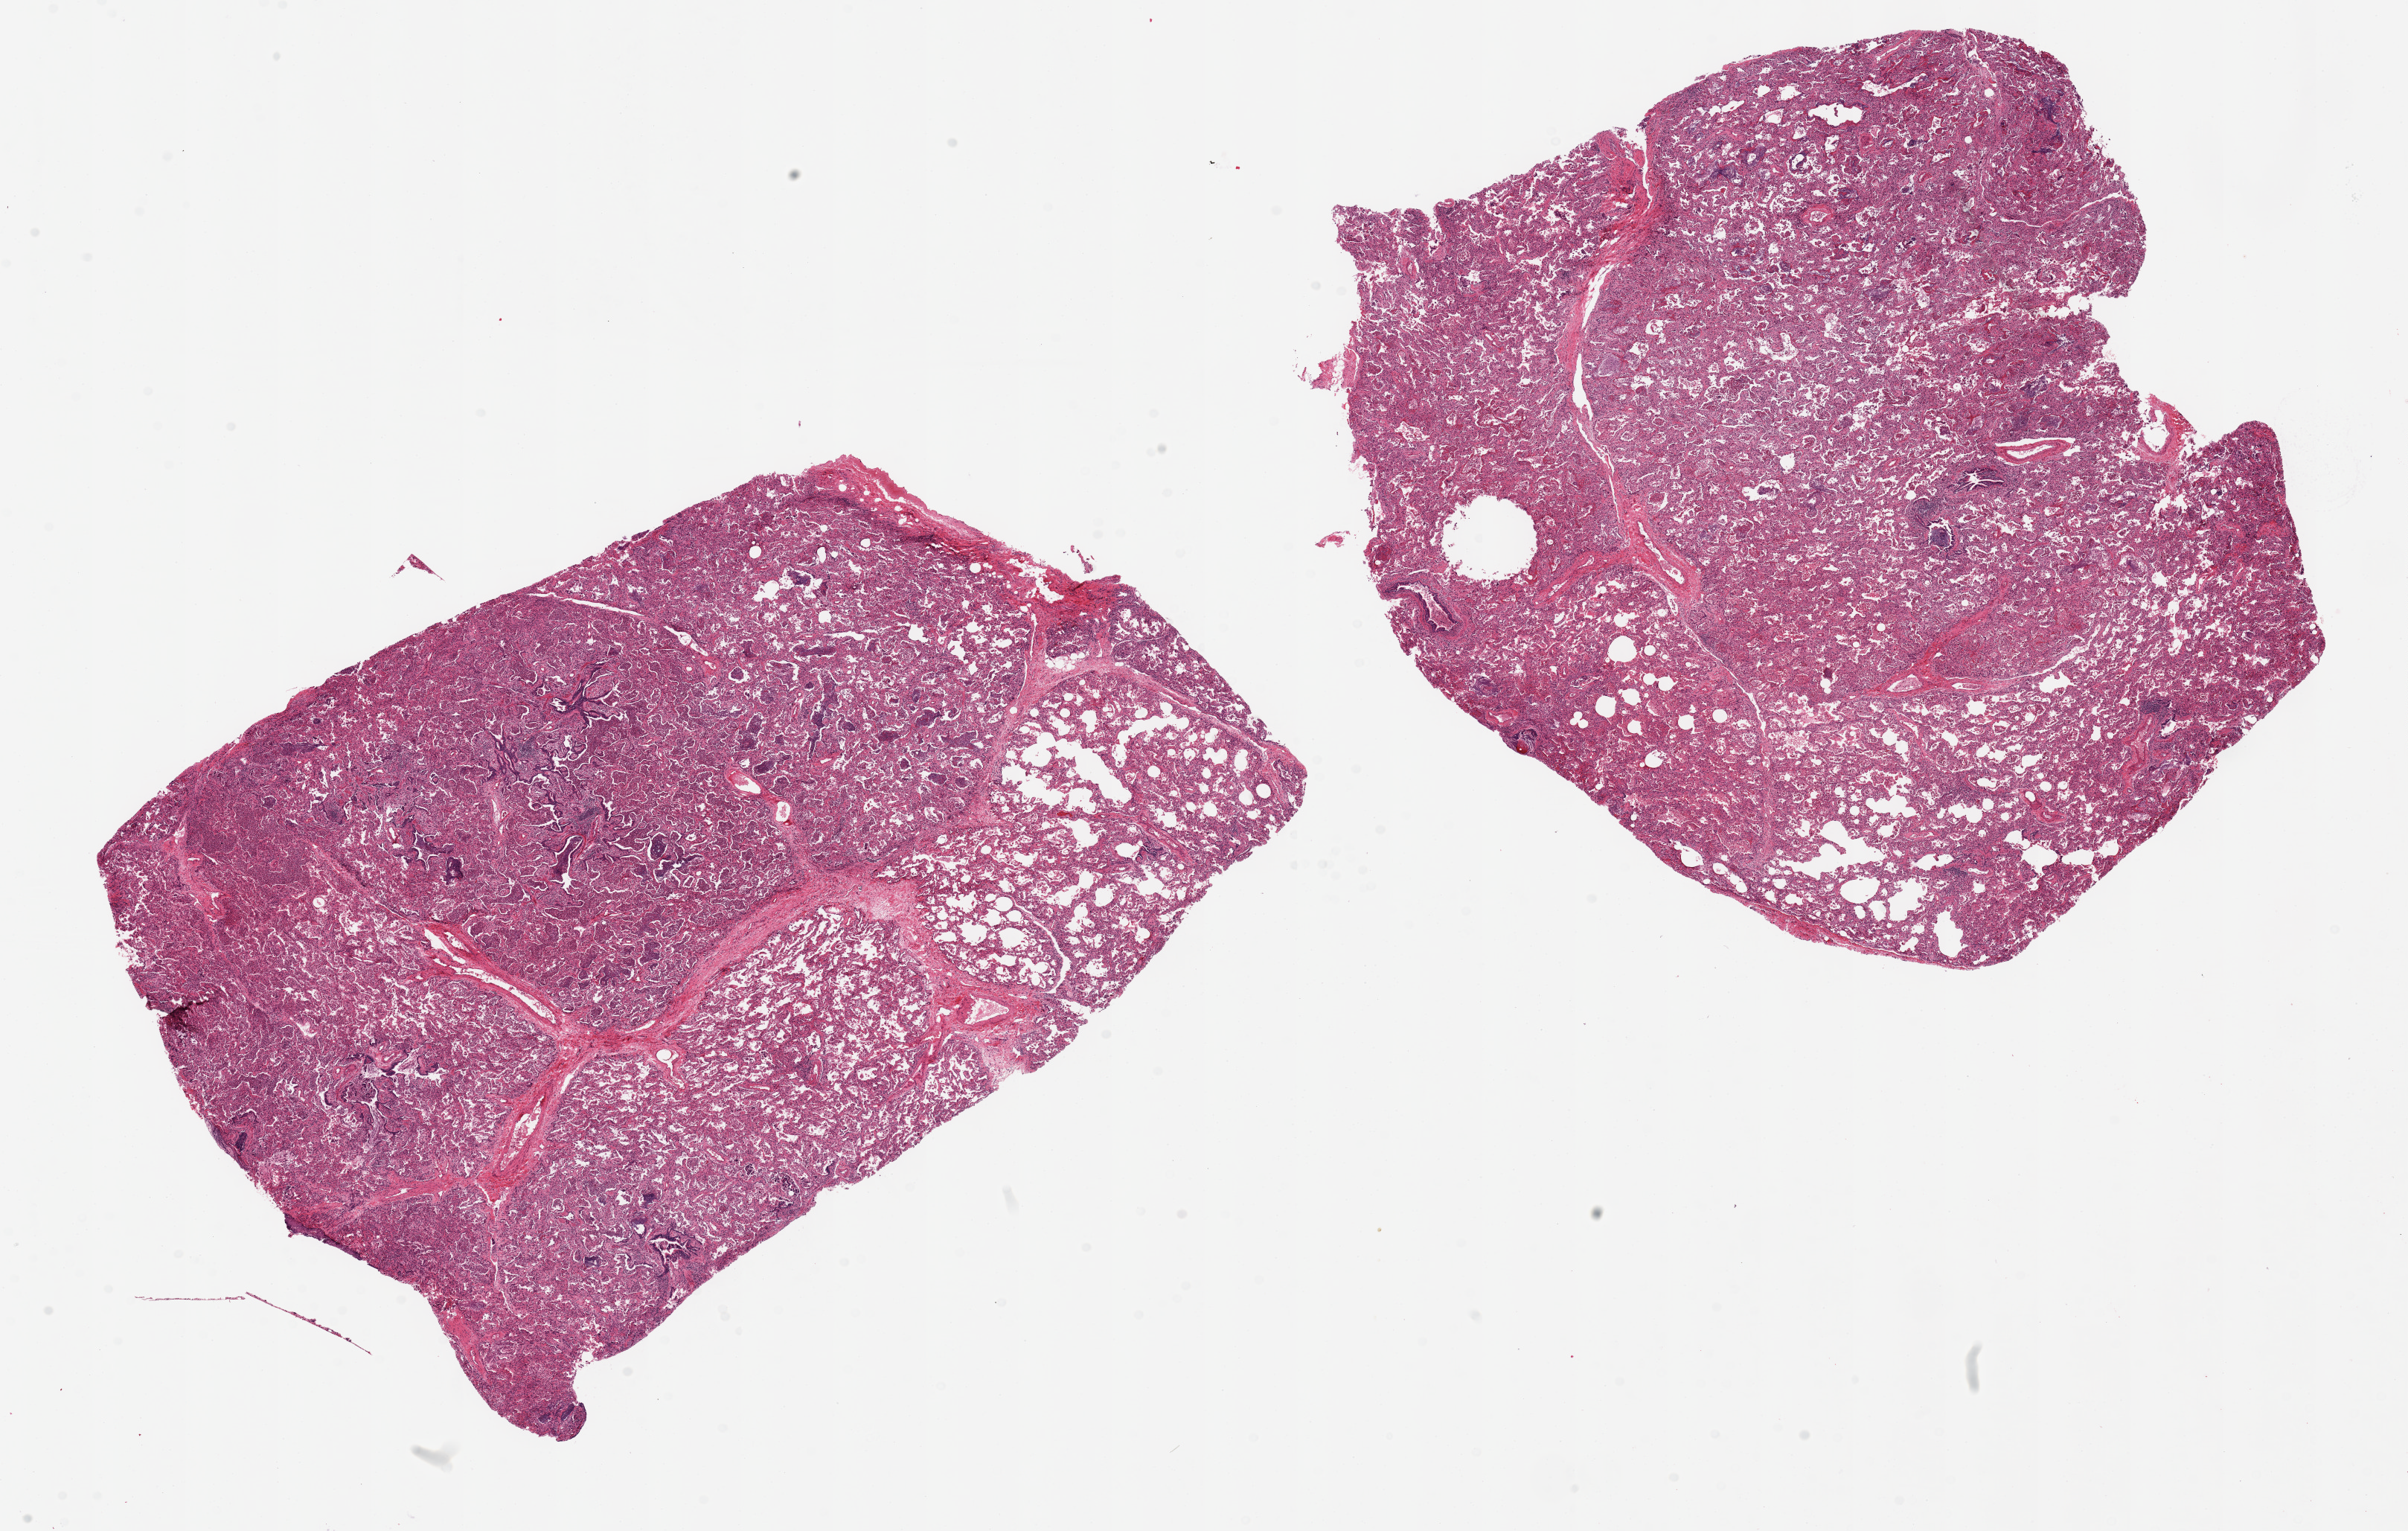
Digitized haematoxylin and eosin-stained section — whole scanned area (about 25.6 x 16.3 mm) shown as a low-resolution overview; PAXgene-fixed paraffin-embedded (PFPE) section; target tissue: lung; tissue donor sample.
- reviewer comment on this tissue sample: 2 pieces 11x87 10x9 mm; Bronchopneumonia in ~40% and interstitial fibrosis in ~60%